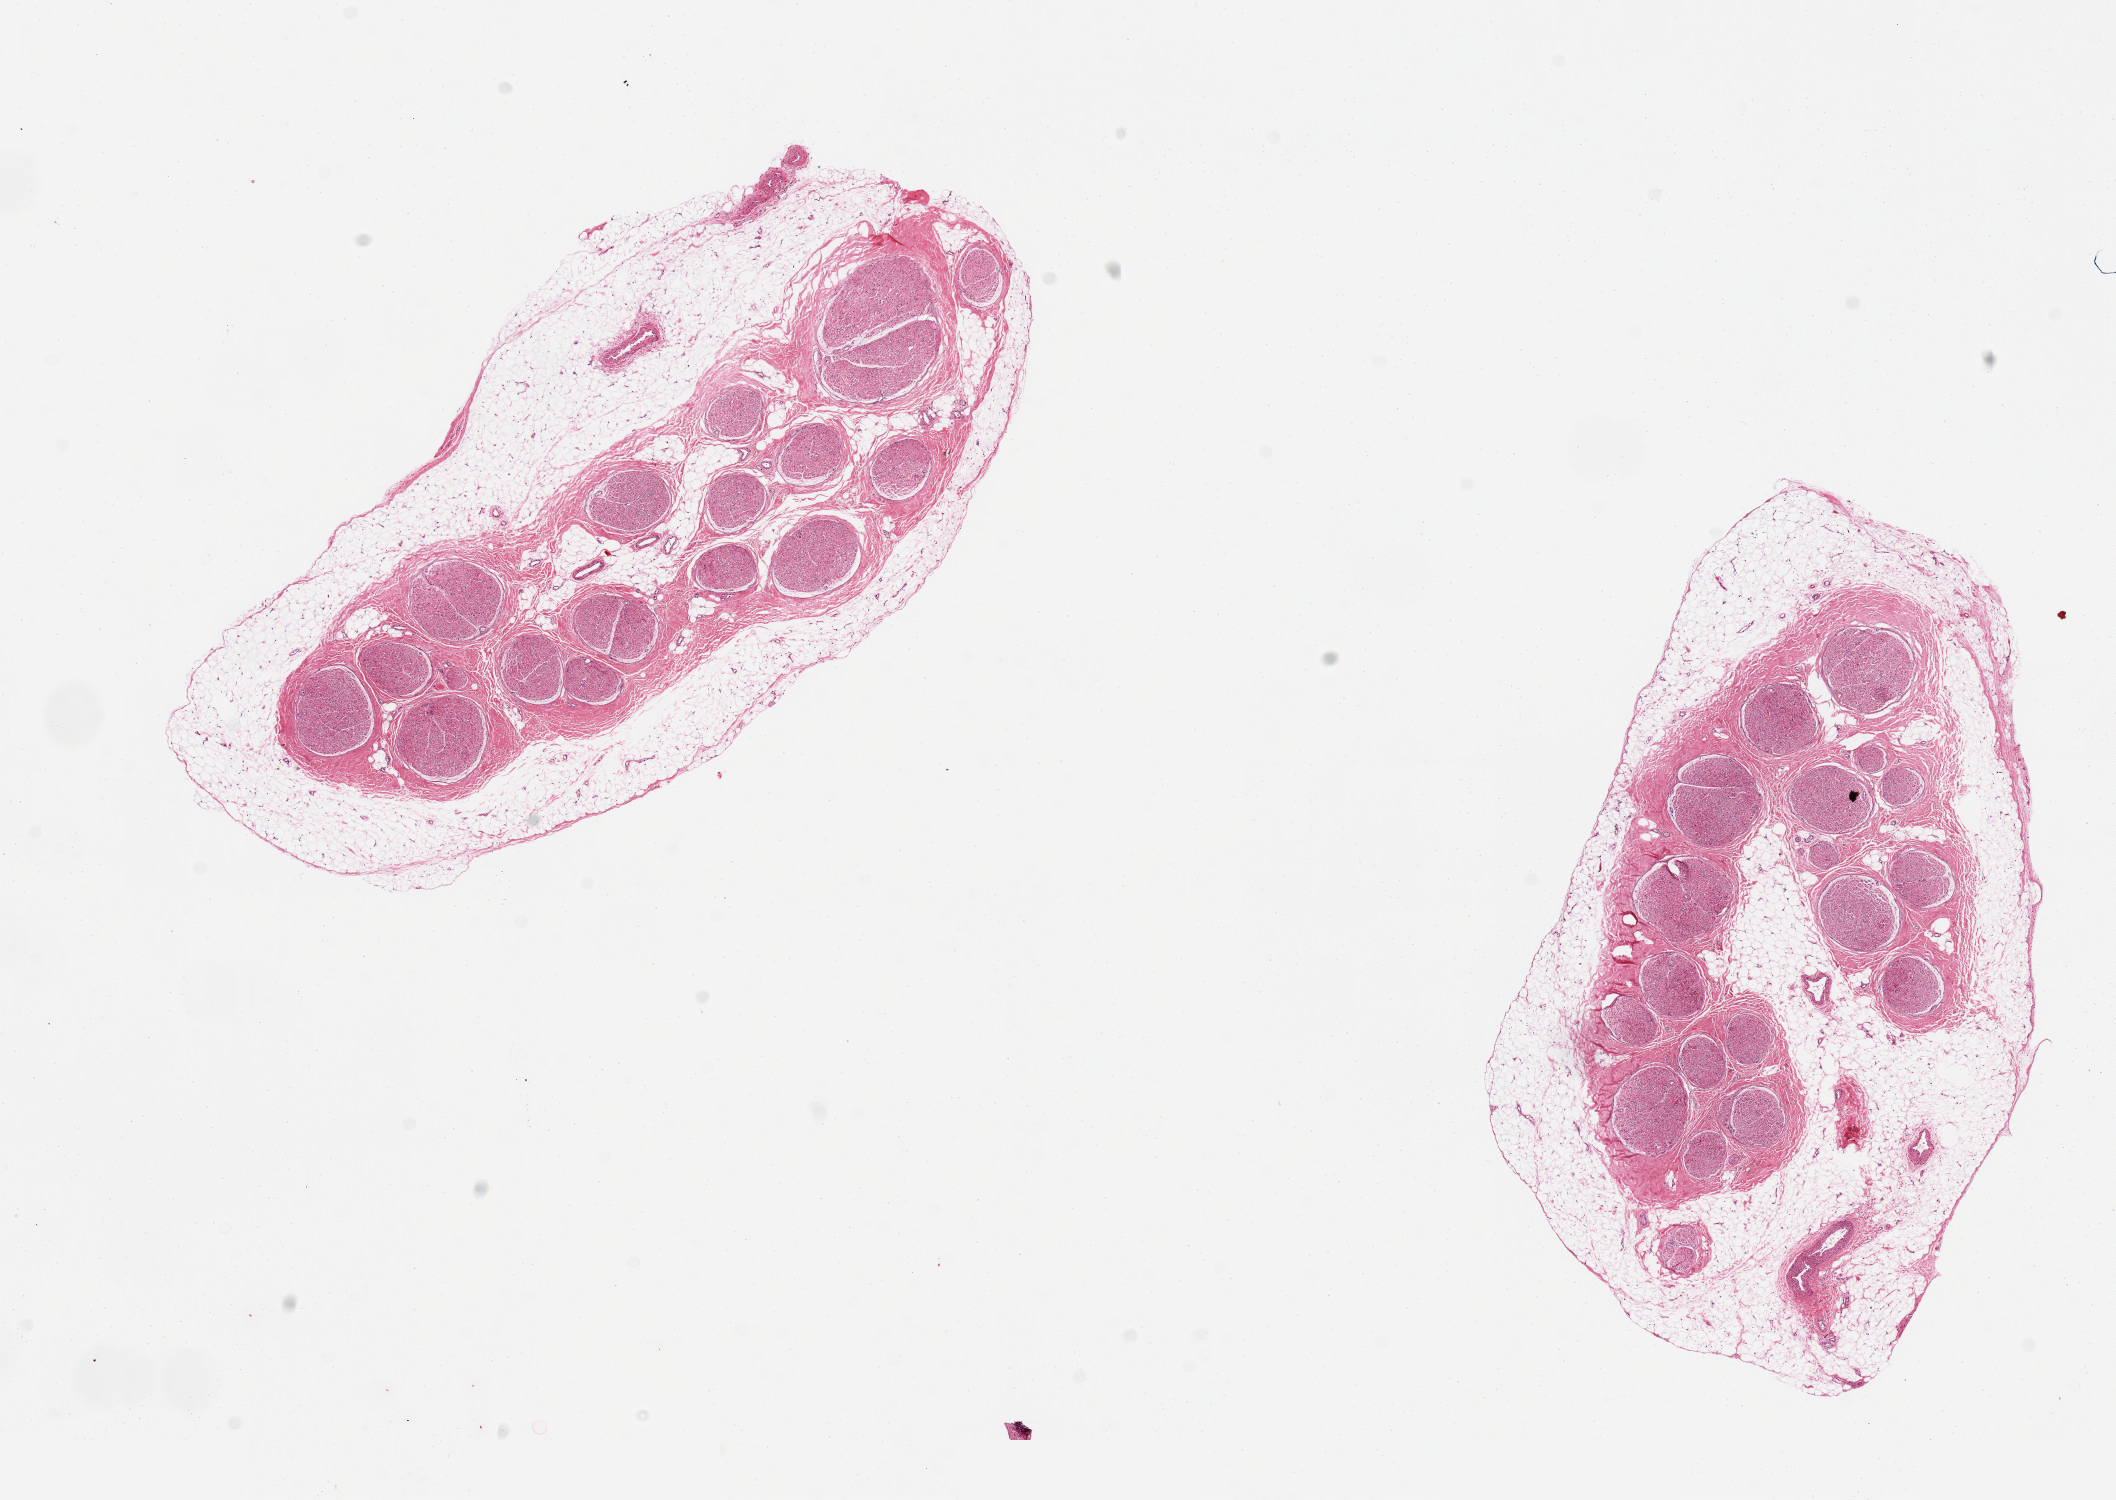
Digitized hematoxylin and eosin (H&E)-stained section — shown as a low-resolution overview of the whole scanned area (about 16.7 x 11.9 mm, from a 20x scan), PAXgene-fixed paraffin-embedded (PFPE) section, target tissue: tibial nerve, donor tissue sample. Donor sex: male.
* review note (as recorded): 2 pieces; 50% mostly external fat